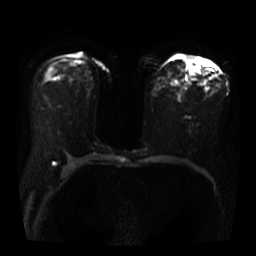
Breast MRI, one axial slice. Slice 20 of 40 in the series (ordered by position). Diffusion-weighted series; image 2 of 4 stored at this slice position (different b-values; order by instance number). 3 T. 256 × 256 image matrix, field of view 360 × 360 mm. Female patient.
Annotated regions visible in this slice (outlined manually by an expert reader):
- tumour on diffusion-weighted imaging: bounding box [x1, y1, x2, y2] px = [185, 59, 198, 74]